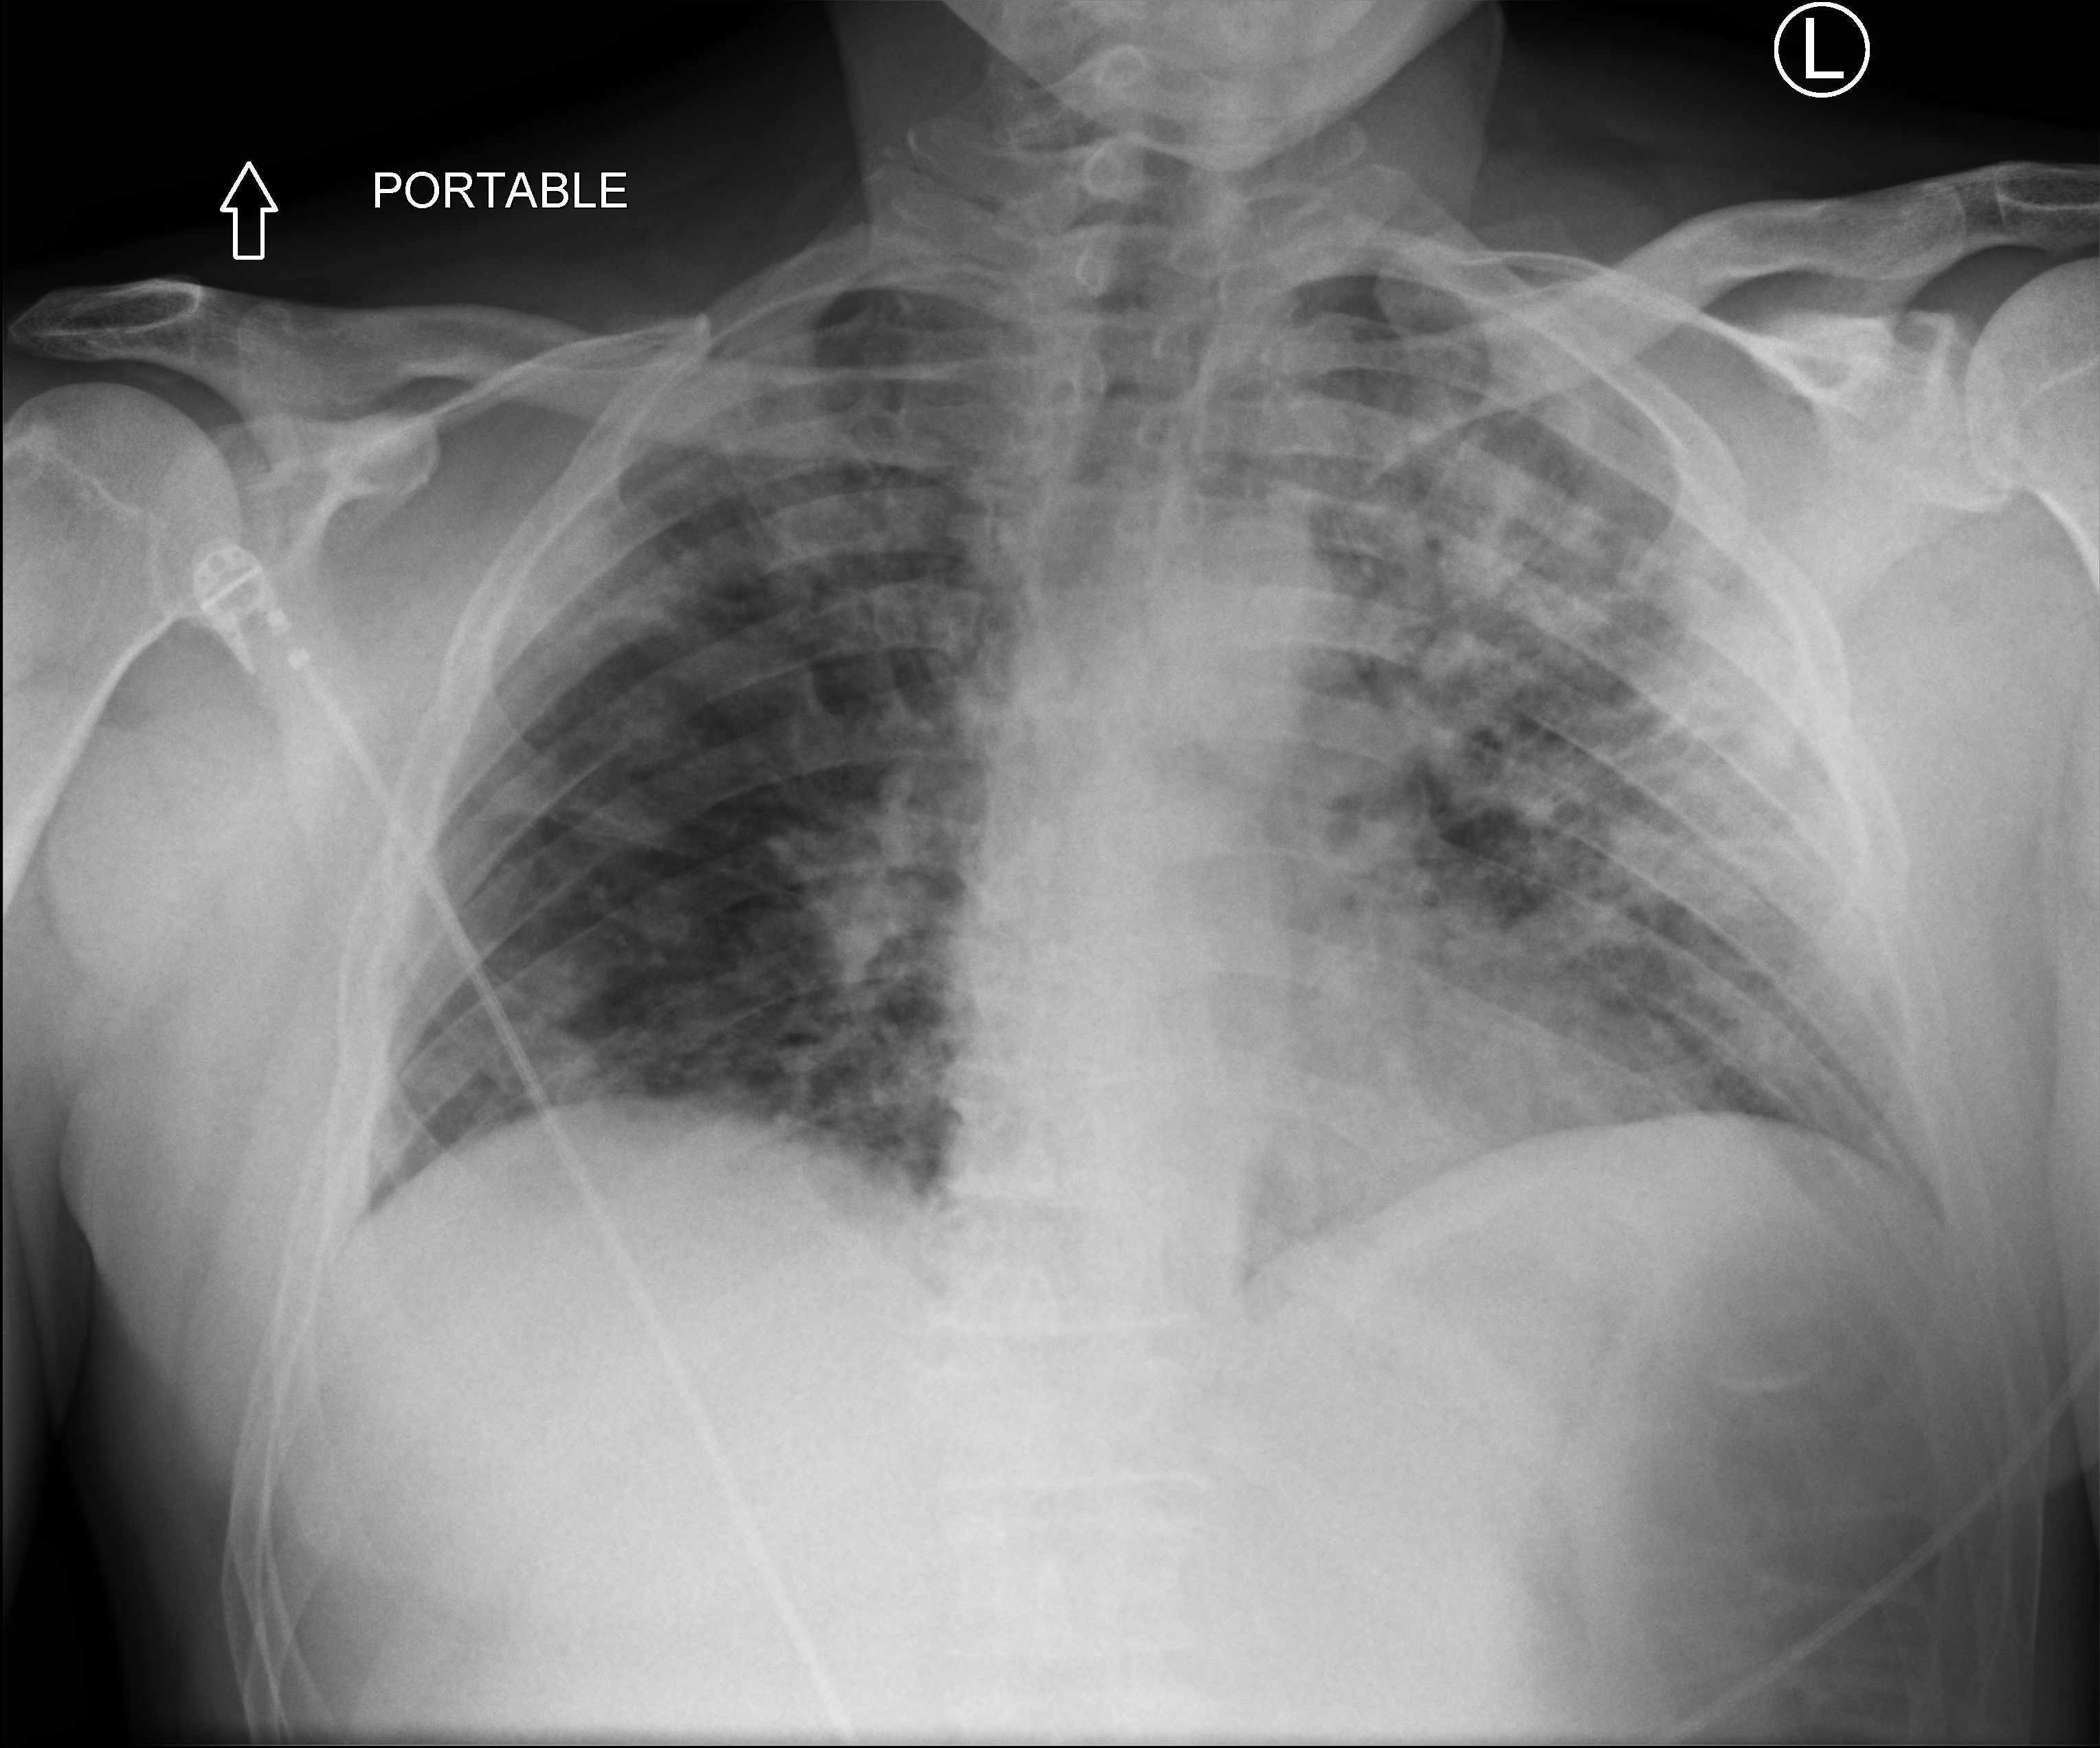
Bedside chest radiograph (computed radiography), anteroposterior (AP) projection. Male patient hospitalised with COVID-19, age 18–59 years.
Hospital-stay facts (about this admission, not read from this image; timing relative to this image not recorded): mechanically ventilated during this hospital stay: no.